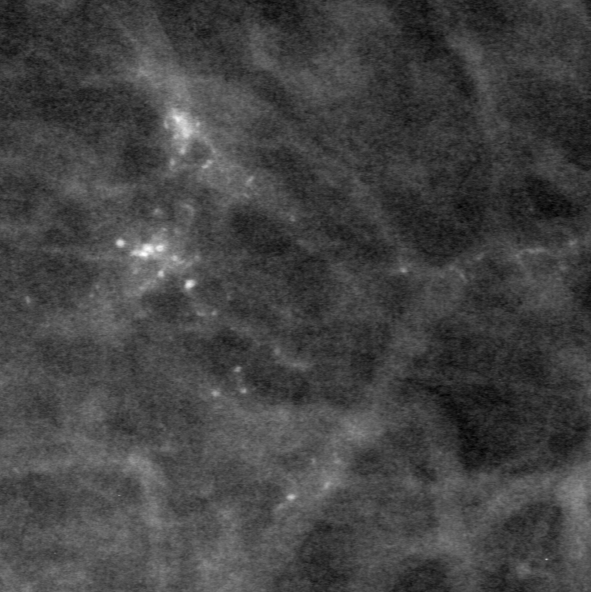
Cropped region of a digitized screen-film mammogram centred on a radiologist-marked abnormality; right breast; CC view; BI-RADS breast density category 2 (scale 1–4).
Finding: calcifications, morphology pleomorphic, distribution segmental; BI-RADS assessment category 4; pathology (as recorded): malignant.